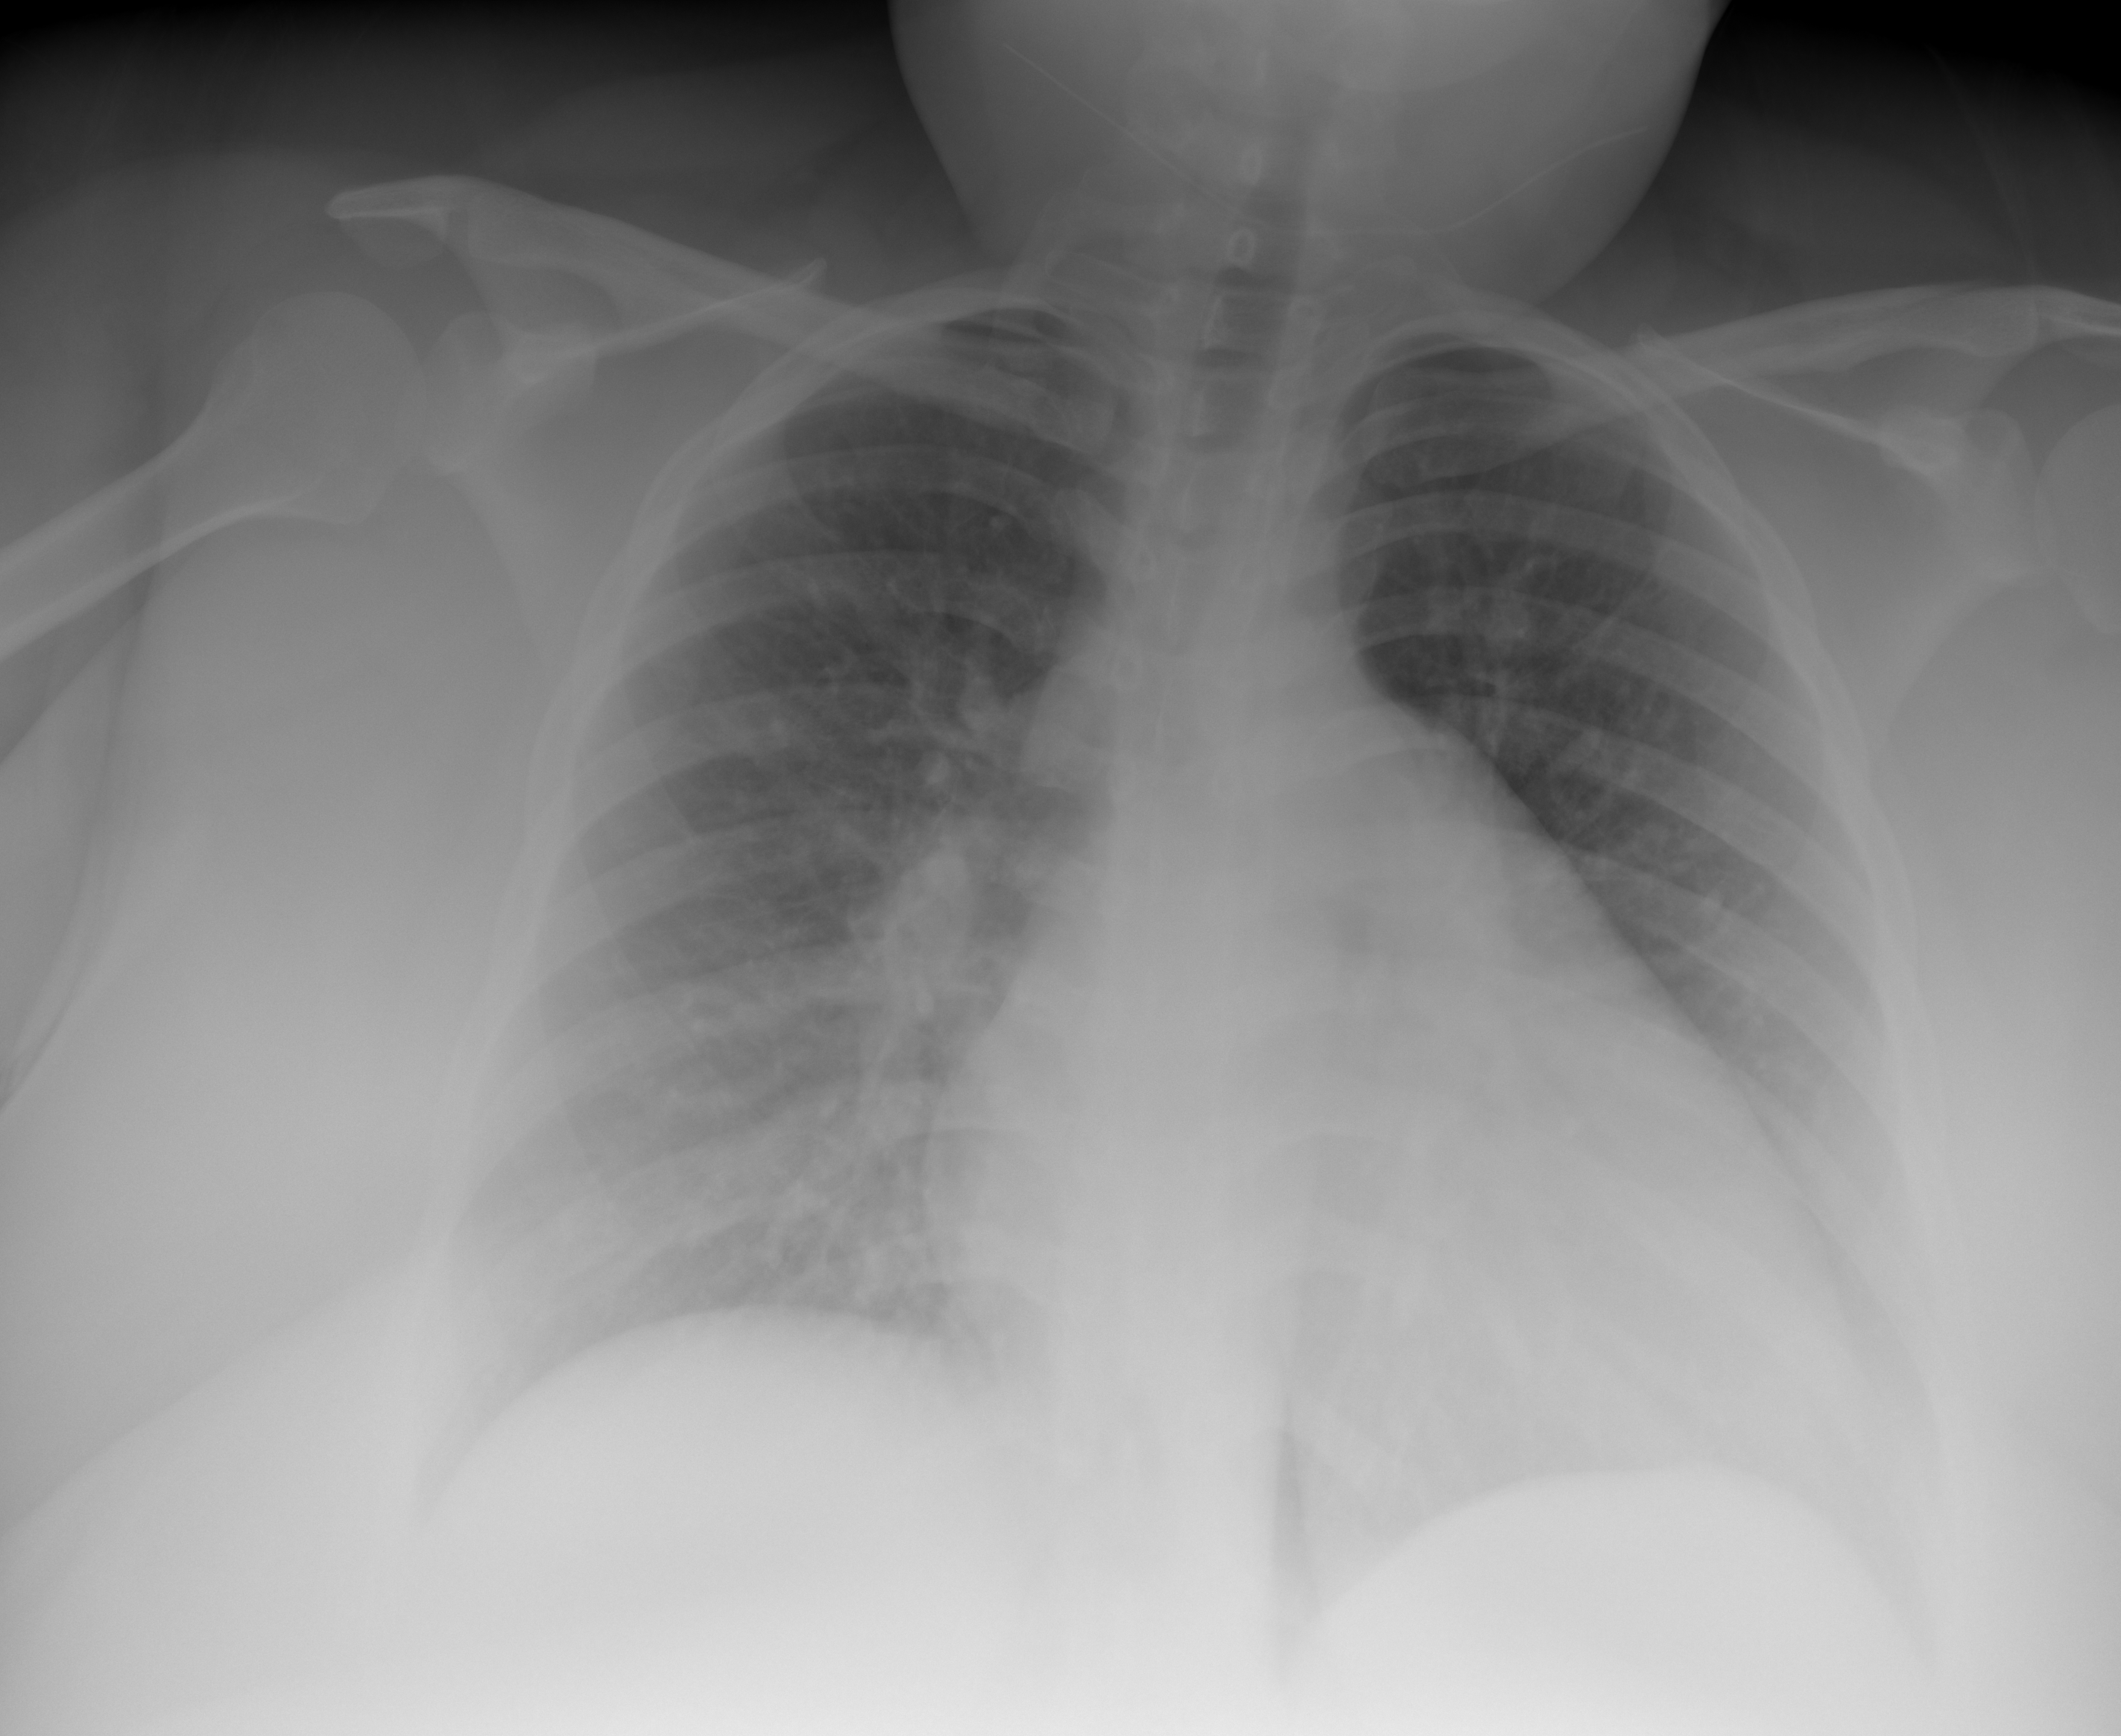
Chest X-ray (portable), AP projection. Female patient, age 22 years; imaged 1 day before the COVID-19 diagnosis.
Radiologist key findings (as recorded): No pleural effusion, pneumothorax or consolidation.